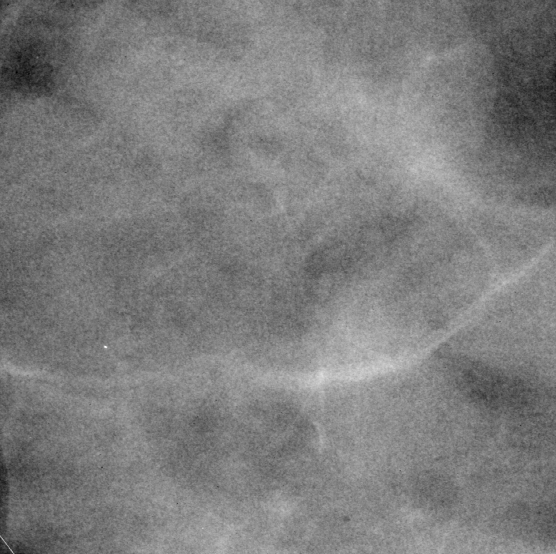
Region of interest cut from a scanned film mammogram (one marked finding); left breast; CC view.
Marked abnormality: mass, shape focal asymmetric density; BI-RADS assessment category 3; pathology result (as recorded, not read from the image): malignant.